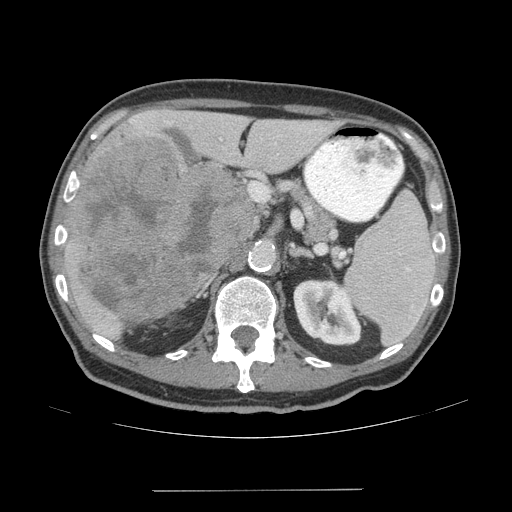
Contrast-enhanced abdominal CT (liver protocol), one axial slice. Position 30 of 77 along the scan axis. Reconstruction kernel STANDARD. 140 kVp. Soft-tissue window (W 400 / L 40 HU). 512 × 512 image matrix. From the clinical record (not read from this slice): diagnosis: hepatocellular carcinoma (patient treated with transarterial chemoembolisation; whether this scan precedes or follows treatment is not stated here); TNM stage (as recorded): Stage-IVA; Child-Pugh class: A; tumour differentiation: well differentiated.
Outlined on this slice (semi-automatic segmentation, software-assisted and operator-edited):
- liver parenchyma outside the tumour (the mass and vessels are separate outlines, so this box may not span the whole liver): box from (x=64, y=108) to (x=336, y=338) px
- mass: (x=70, y=139)–(x=255, y=320)